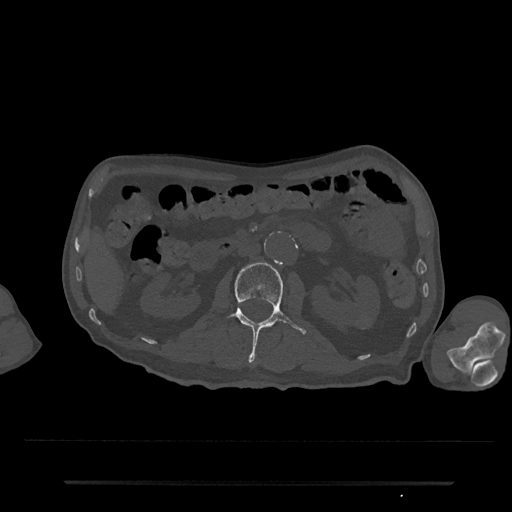
CT including the spine, one axial slice. Position 61 of 797 along the scan axis. Reconstruction kernel Br40s/3. Bone window (W 1800 / L 400 HU). 0.5 mm slice thickness. 512 × 512 image matrix. Male patient, age 74 years. Case-level facts recorded for this patient, not image findings: primary cancer: prostate.
Structures marked on this image (semi-automatically segmented with operator editing):
- L2 vertebra: bounding box (x1, y1, x2, y2) in pixels: (225, 262, 307, 362)